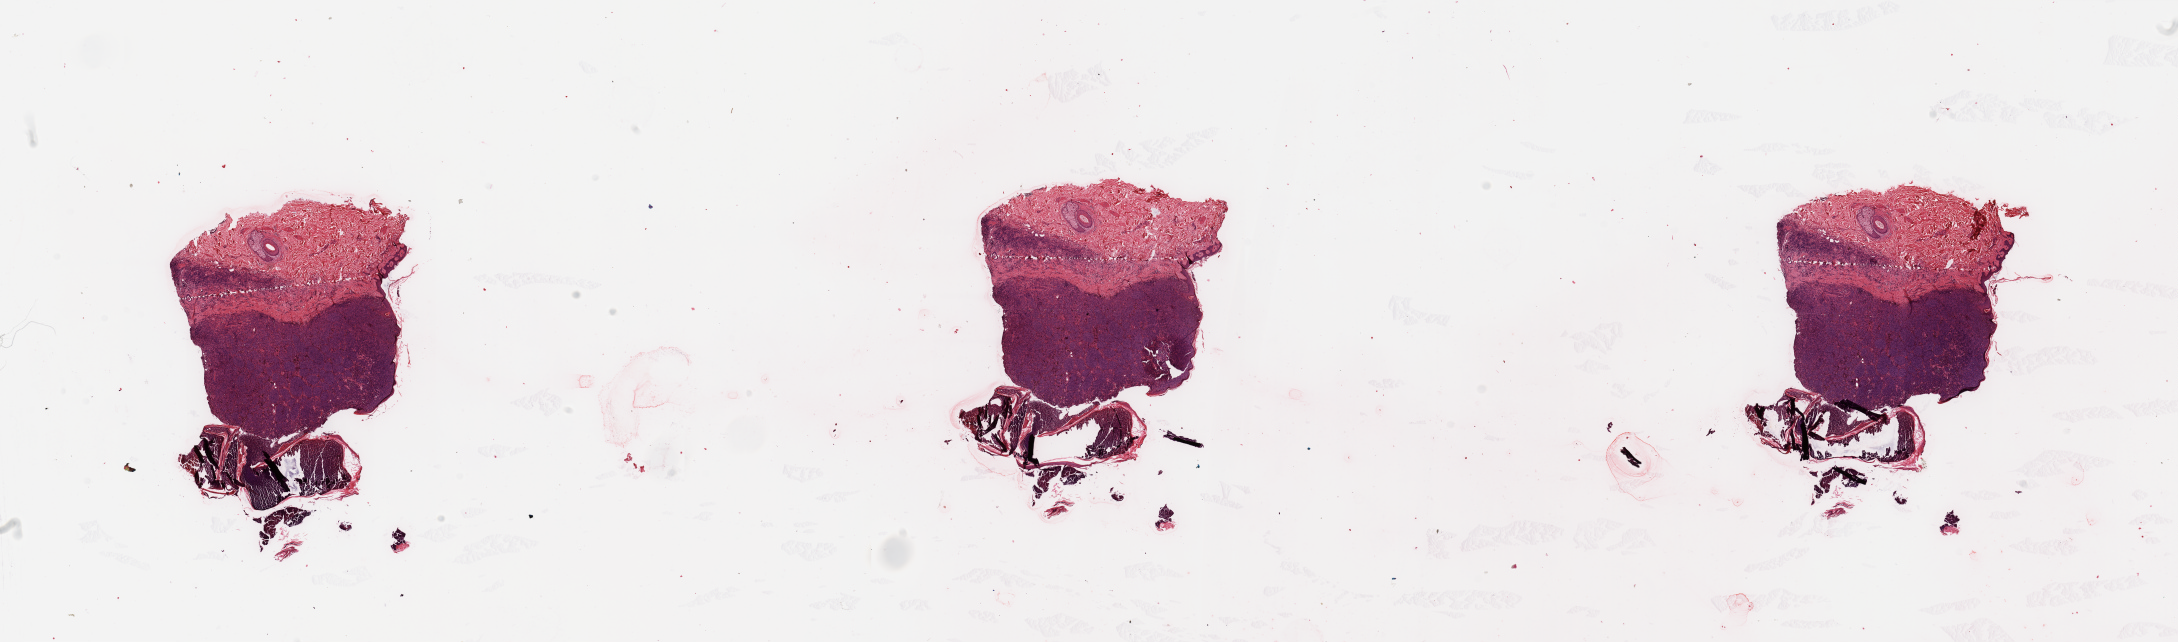
Digitized H&E tissue section (whole slide) — shown as a low-resolution overview of the whole scanned area (about 34.5 x 10.2 mm); tumour tissue sample, sampled site: trunk. Male, 69 y/o. Slide review estimates, as recorded: tumour nuclei 90%, necrosis 0%.
Primary tumour site (as recorded): trunk. AJCC pathologic stage: IIA. Histologic diagnosis: Malignant melanoma, NOS.